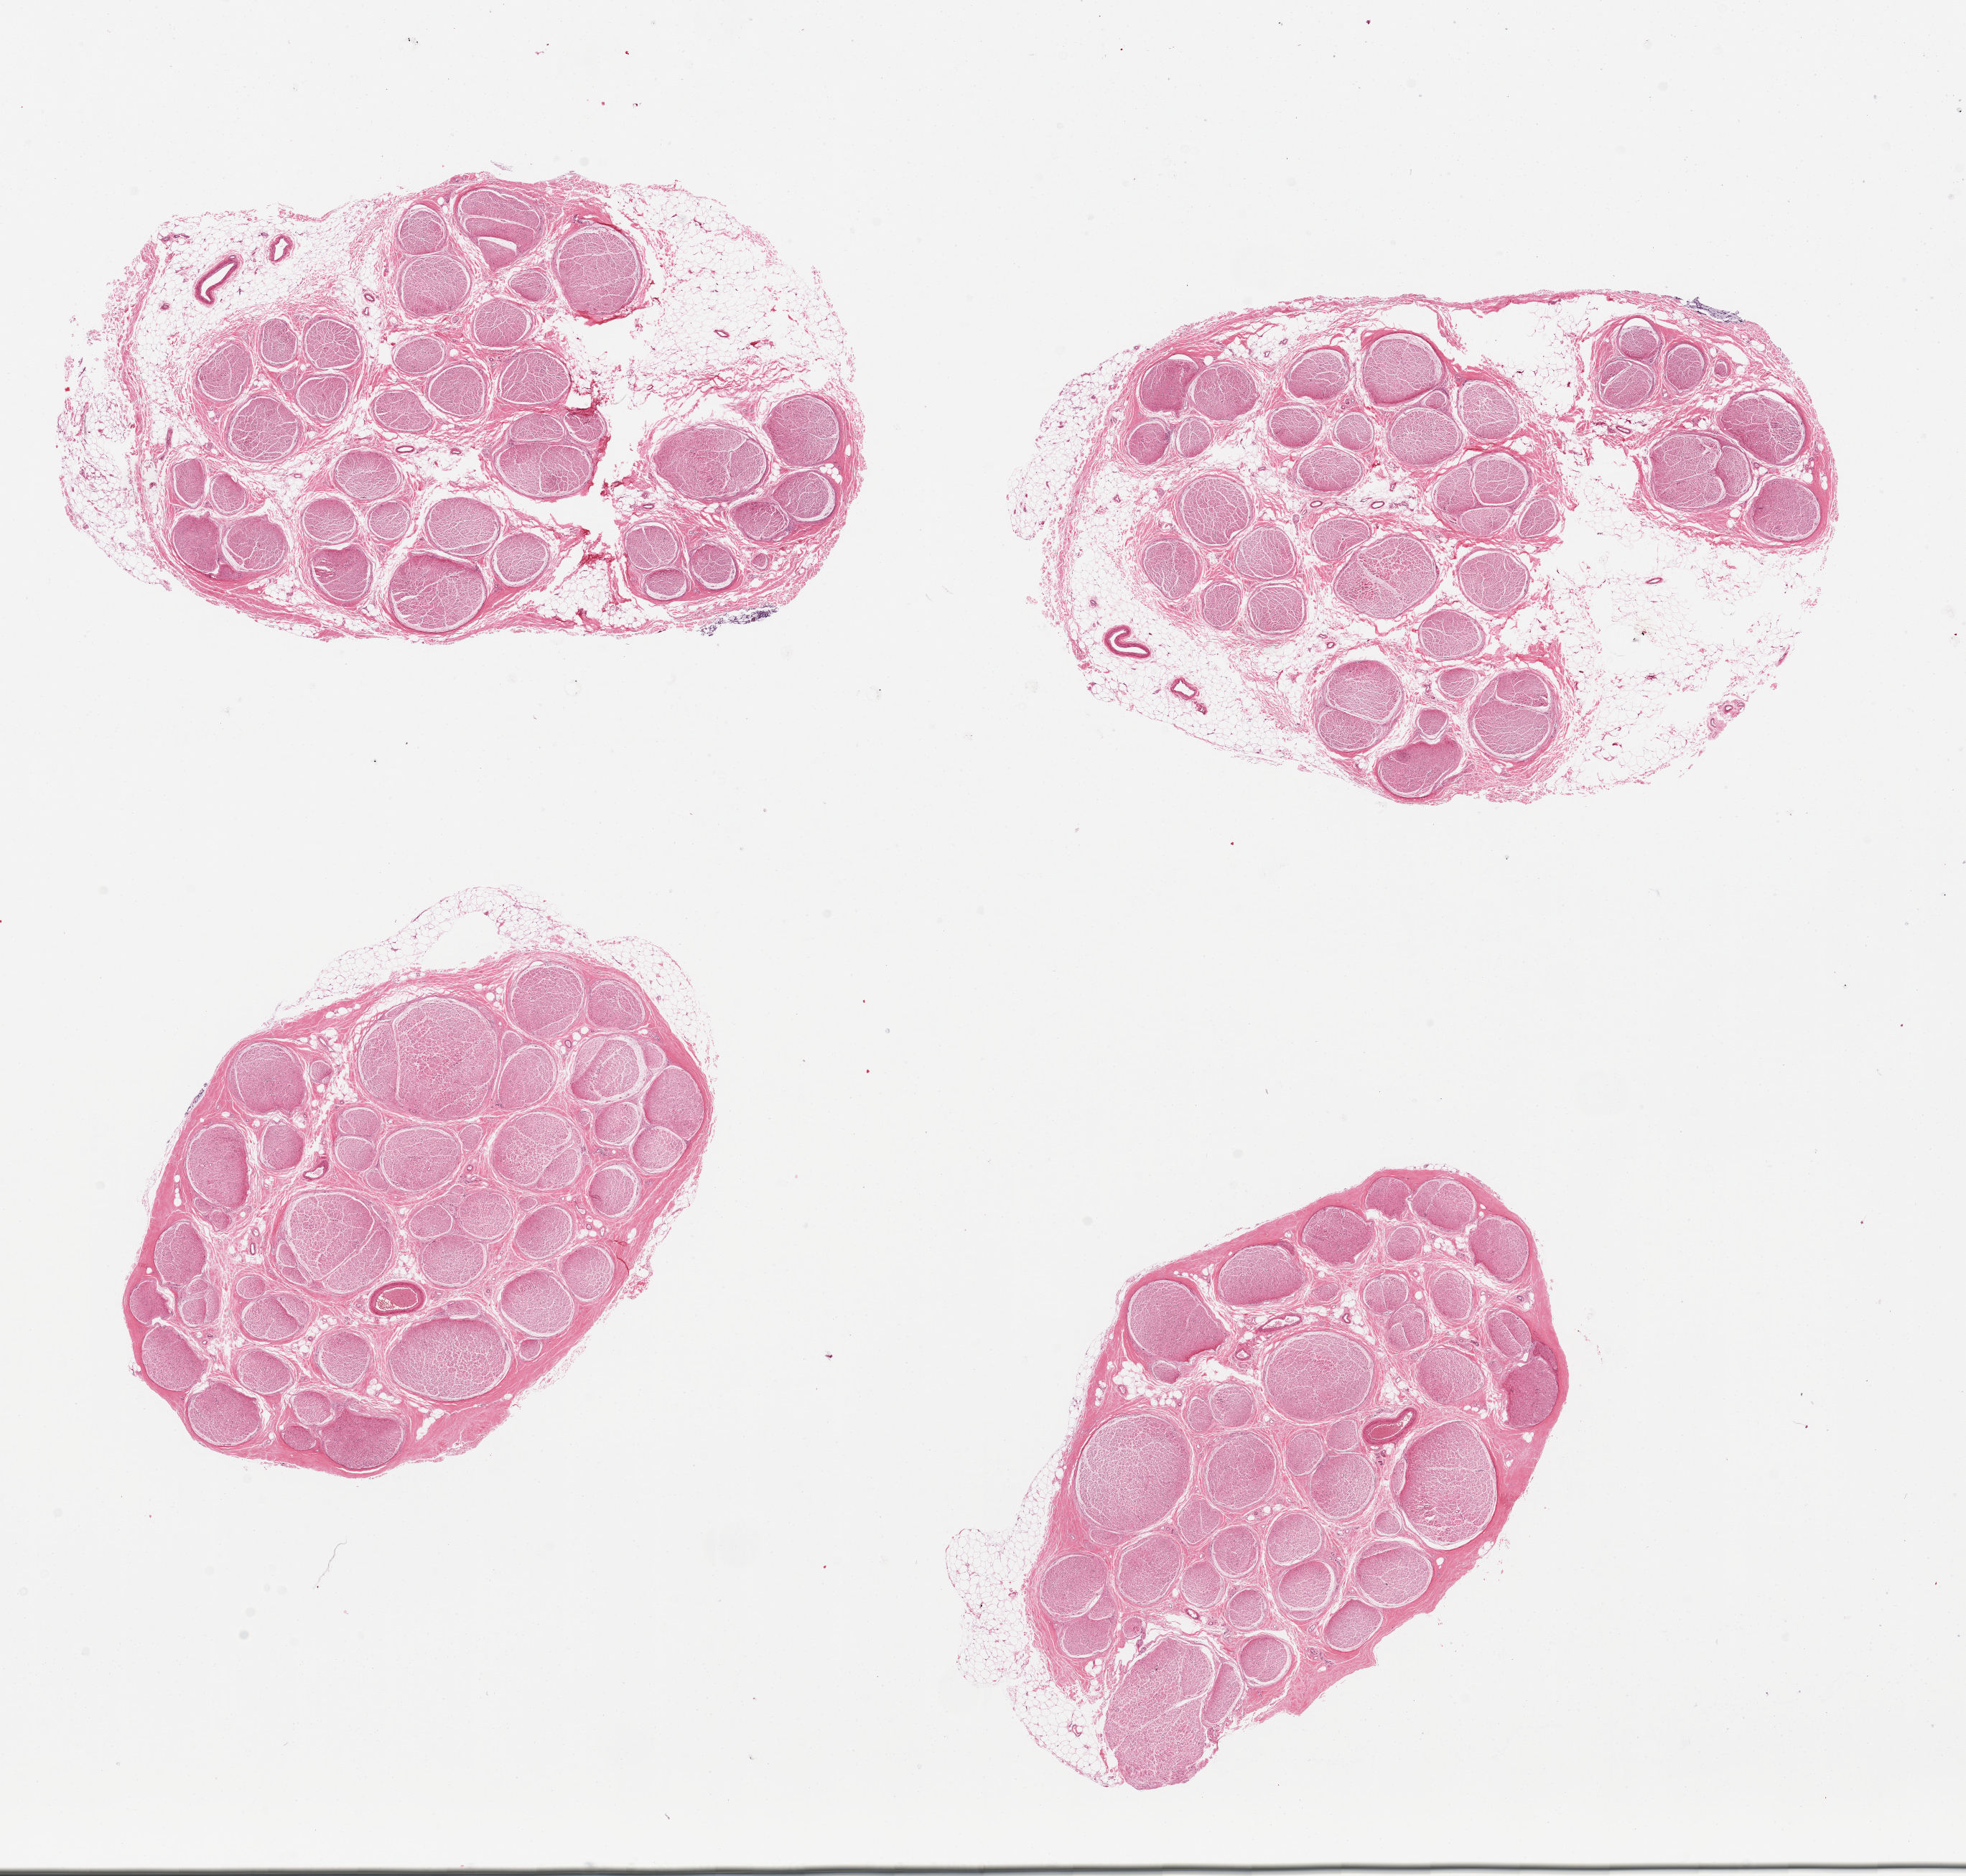
Haematoxylin and eosin whole-slide image, brightfield, shown as a low-resolution overview of the whole scanned area (about 21.7 x 20.7 mm). PAXgene-fixed paraffin-embedded (PFPE) section. Section of tibial nerve (target tissue). Tissue donor sample. Male donor.
Review note (as recorded): 4 pieces: 2 are fat free, 2 with 30-40% fat.